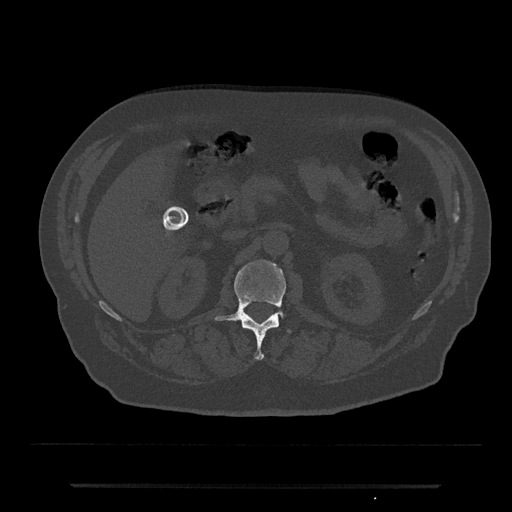
CT including the spine, one axial slice; position 530 of 797 along the scan axis; 120 kVp; bone window (W 1800 / L 400 HU); 512 × 512 image matrix. Patient: male, 80 years. From the clinical record (not read from this slice): primary cancer: prostate; vertebrae with lytic lesions (as recorded): L1, T11.
Structures marked on this image (semi-automatically segmented with operator editing):
- L1 vertebra: bounding box <215,259,287,360> (left, top, right, bottom; pixels)